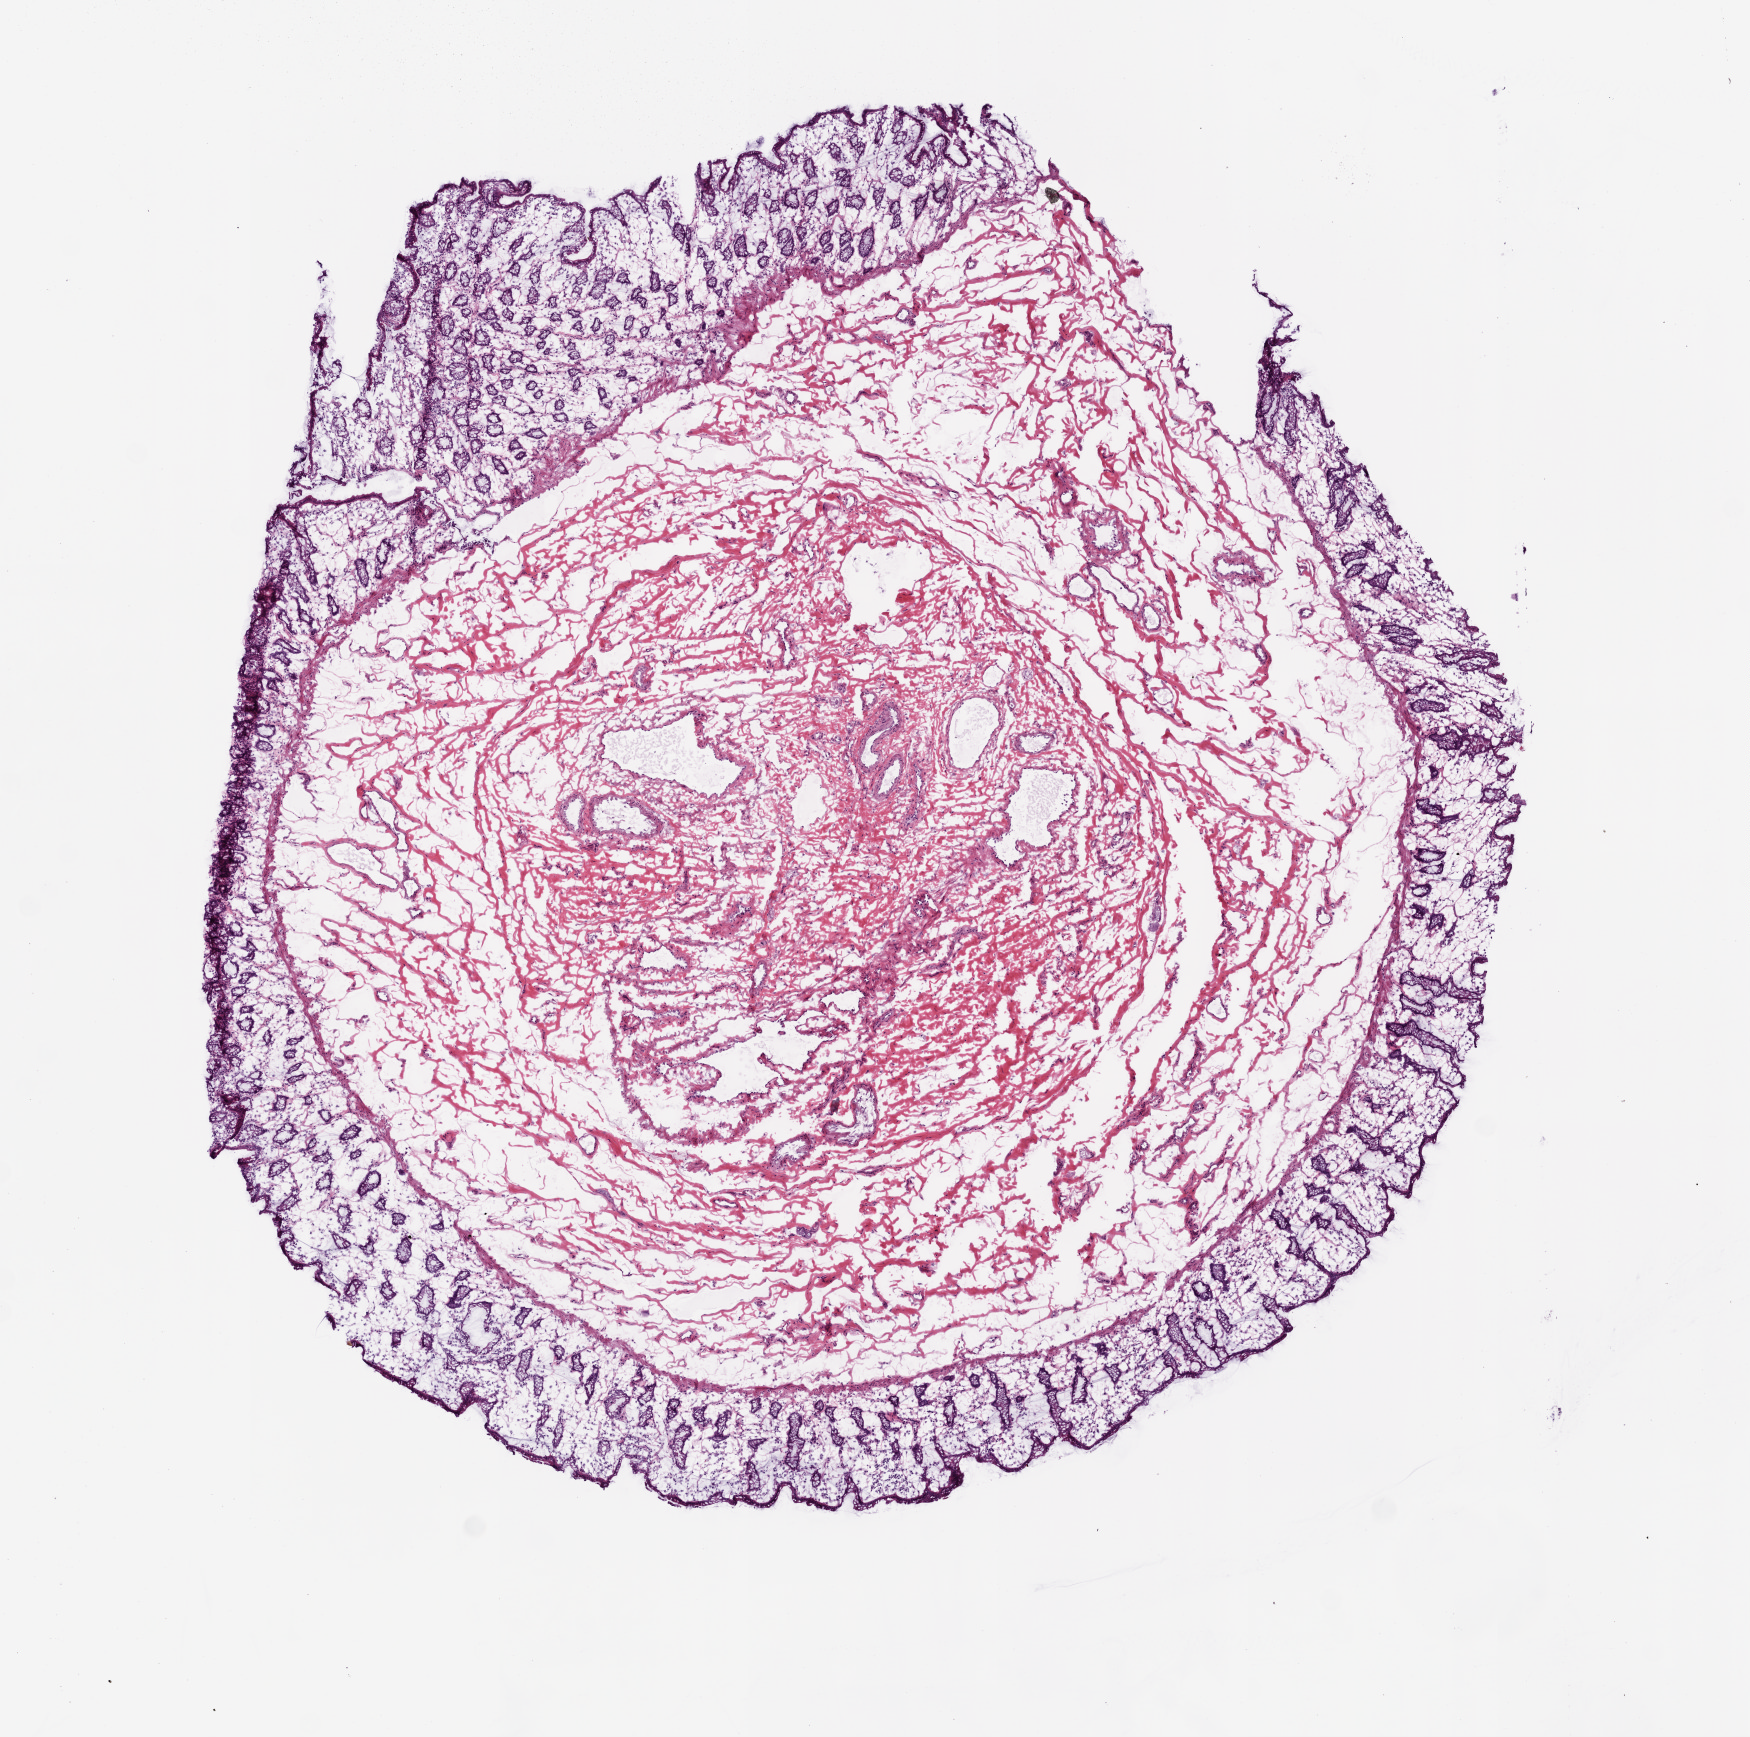
Digitized H&E tissue section (whole slide) — whole scanned area (about 7.0 x 7.0 mm) shown as a low-resolution overview. Frozen section from the top of the tissue portion. Colon, solid tissue normal (non-tumour tissue) sample. Patient sex: female.
- this section: solid tissue normal sample (biorepository sample class)
- patient diagnosis: Adenocarcinoma, NOS (ascending colon)